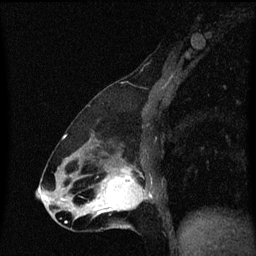
Breast MRI (dynamic contrast-enhanced), one sagittal slice; position 28 of 60 along the scan axis; dynamic contrast-enhanced series, image 2 of 3 at this slice position (ordered by acquisition); 1.5 T; TE 4.2 ms, TR 8.4 ms; 256 × 256 image matrix, field of view 200 × 200 mm. Patient: female, 47 years.
Annotated regions visible in this slice (semi-automatically segmented with operator editing):
- analysis volume of interest (the breast-tissue region the enhancement analysis was run in; not a lesion): bounding box [x1, y1, x2, y2] px = [100, 172, 151, 217]
- tumour enhancement mask (voxels above the 70 % enhancement threshold inside the analysis volume of interest): [100, 172, 147, 215]